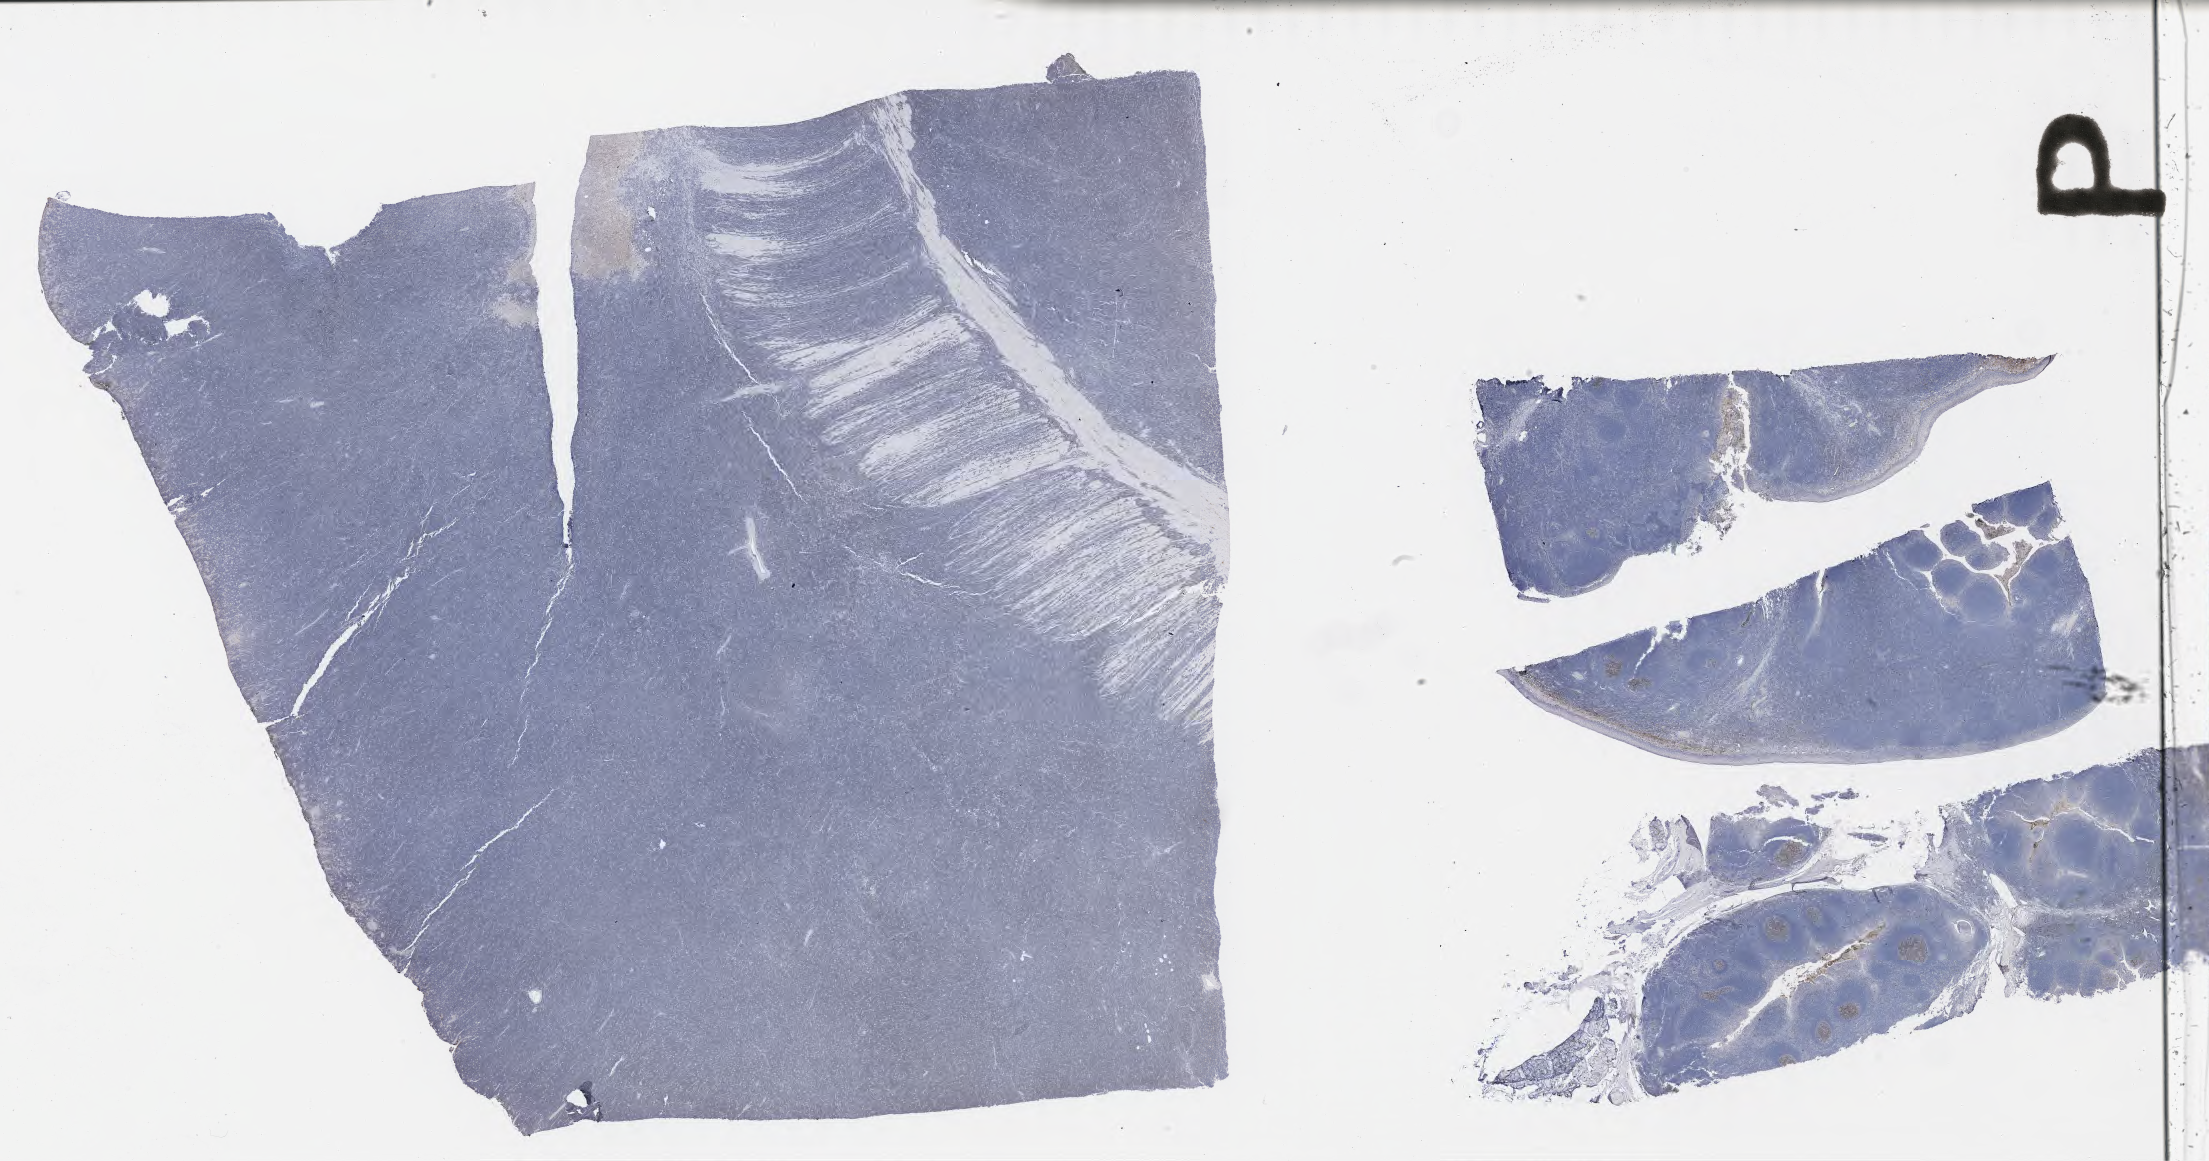
IHC for CD10, whole-slide image, a low-resolution overview of the entire scanned area, about 35.7 x 18.8 mm. Specimen: tumor tissue. Anatomic site: colon. Male patient, age 14 years.
Diagnosis: Burkitt lymphoma, NOS.